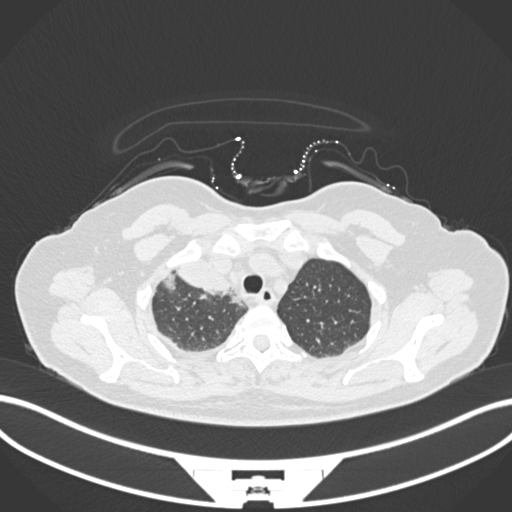
Chest CT, one axial slice; slice 141 of 172 in the series (ordered by position); reconstruction kernel B30f; lung window (W 1500 / L -600 HU); 512 × 512 image matrix, field of view 400 × 400 mm. Patient: female, 52 years. Case-level facts recorded for this patient, not image findings: clinical TNM (as recorded): T3 N1 M1.
Outlined on this slice (bounding box drawn by a radiologist):
- lung tumour (recorded histology: adenocarcinoma): box from (x=176, y=261) to (x=237, y=300) px